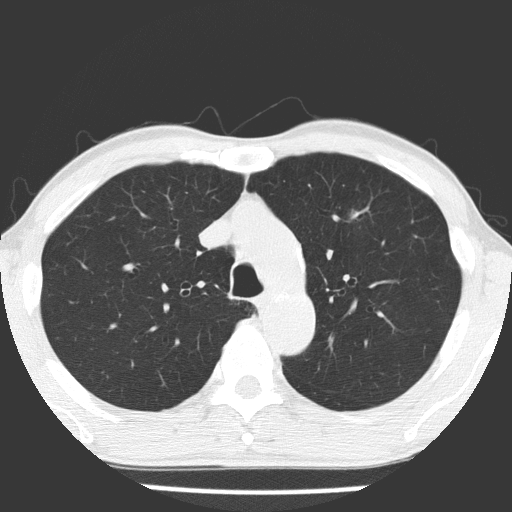
Low-dose screening chest CT, axial slice. Baseline annual screen. Lung window (W 1500 / L -600 HU). 2 mm slice thickness. 120 kVp. Slice 53 of 177 in the series. Male, age 66 years at enrolment. Current smoker at enrolment.
Expert reader's lesion annotation, box from (x=328, y=193) to (x=377, y=239) px. The exam's reader record, not a measurement of the box and not confirmed to be the same lesion: non-calcified nodule or mass ≥4 mm, left upper lobe, 8 × 8 mm, poorly defined margins, mixed attenuation.